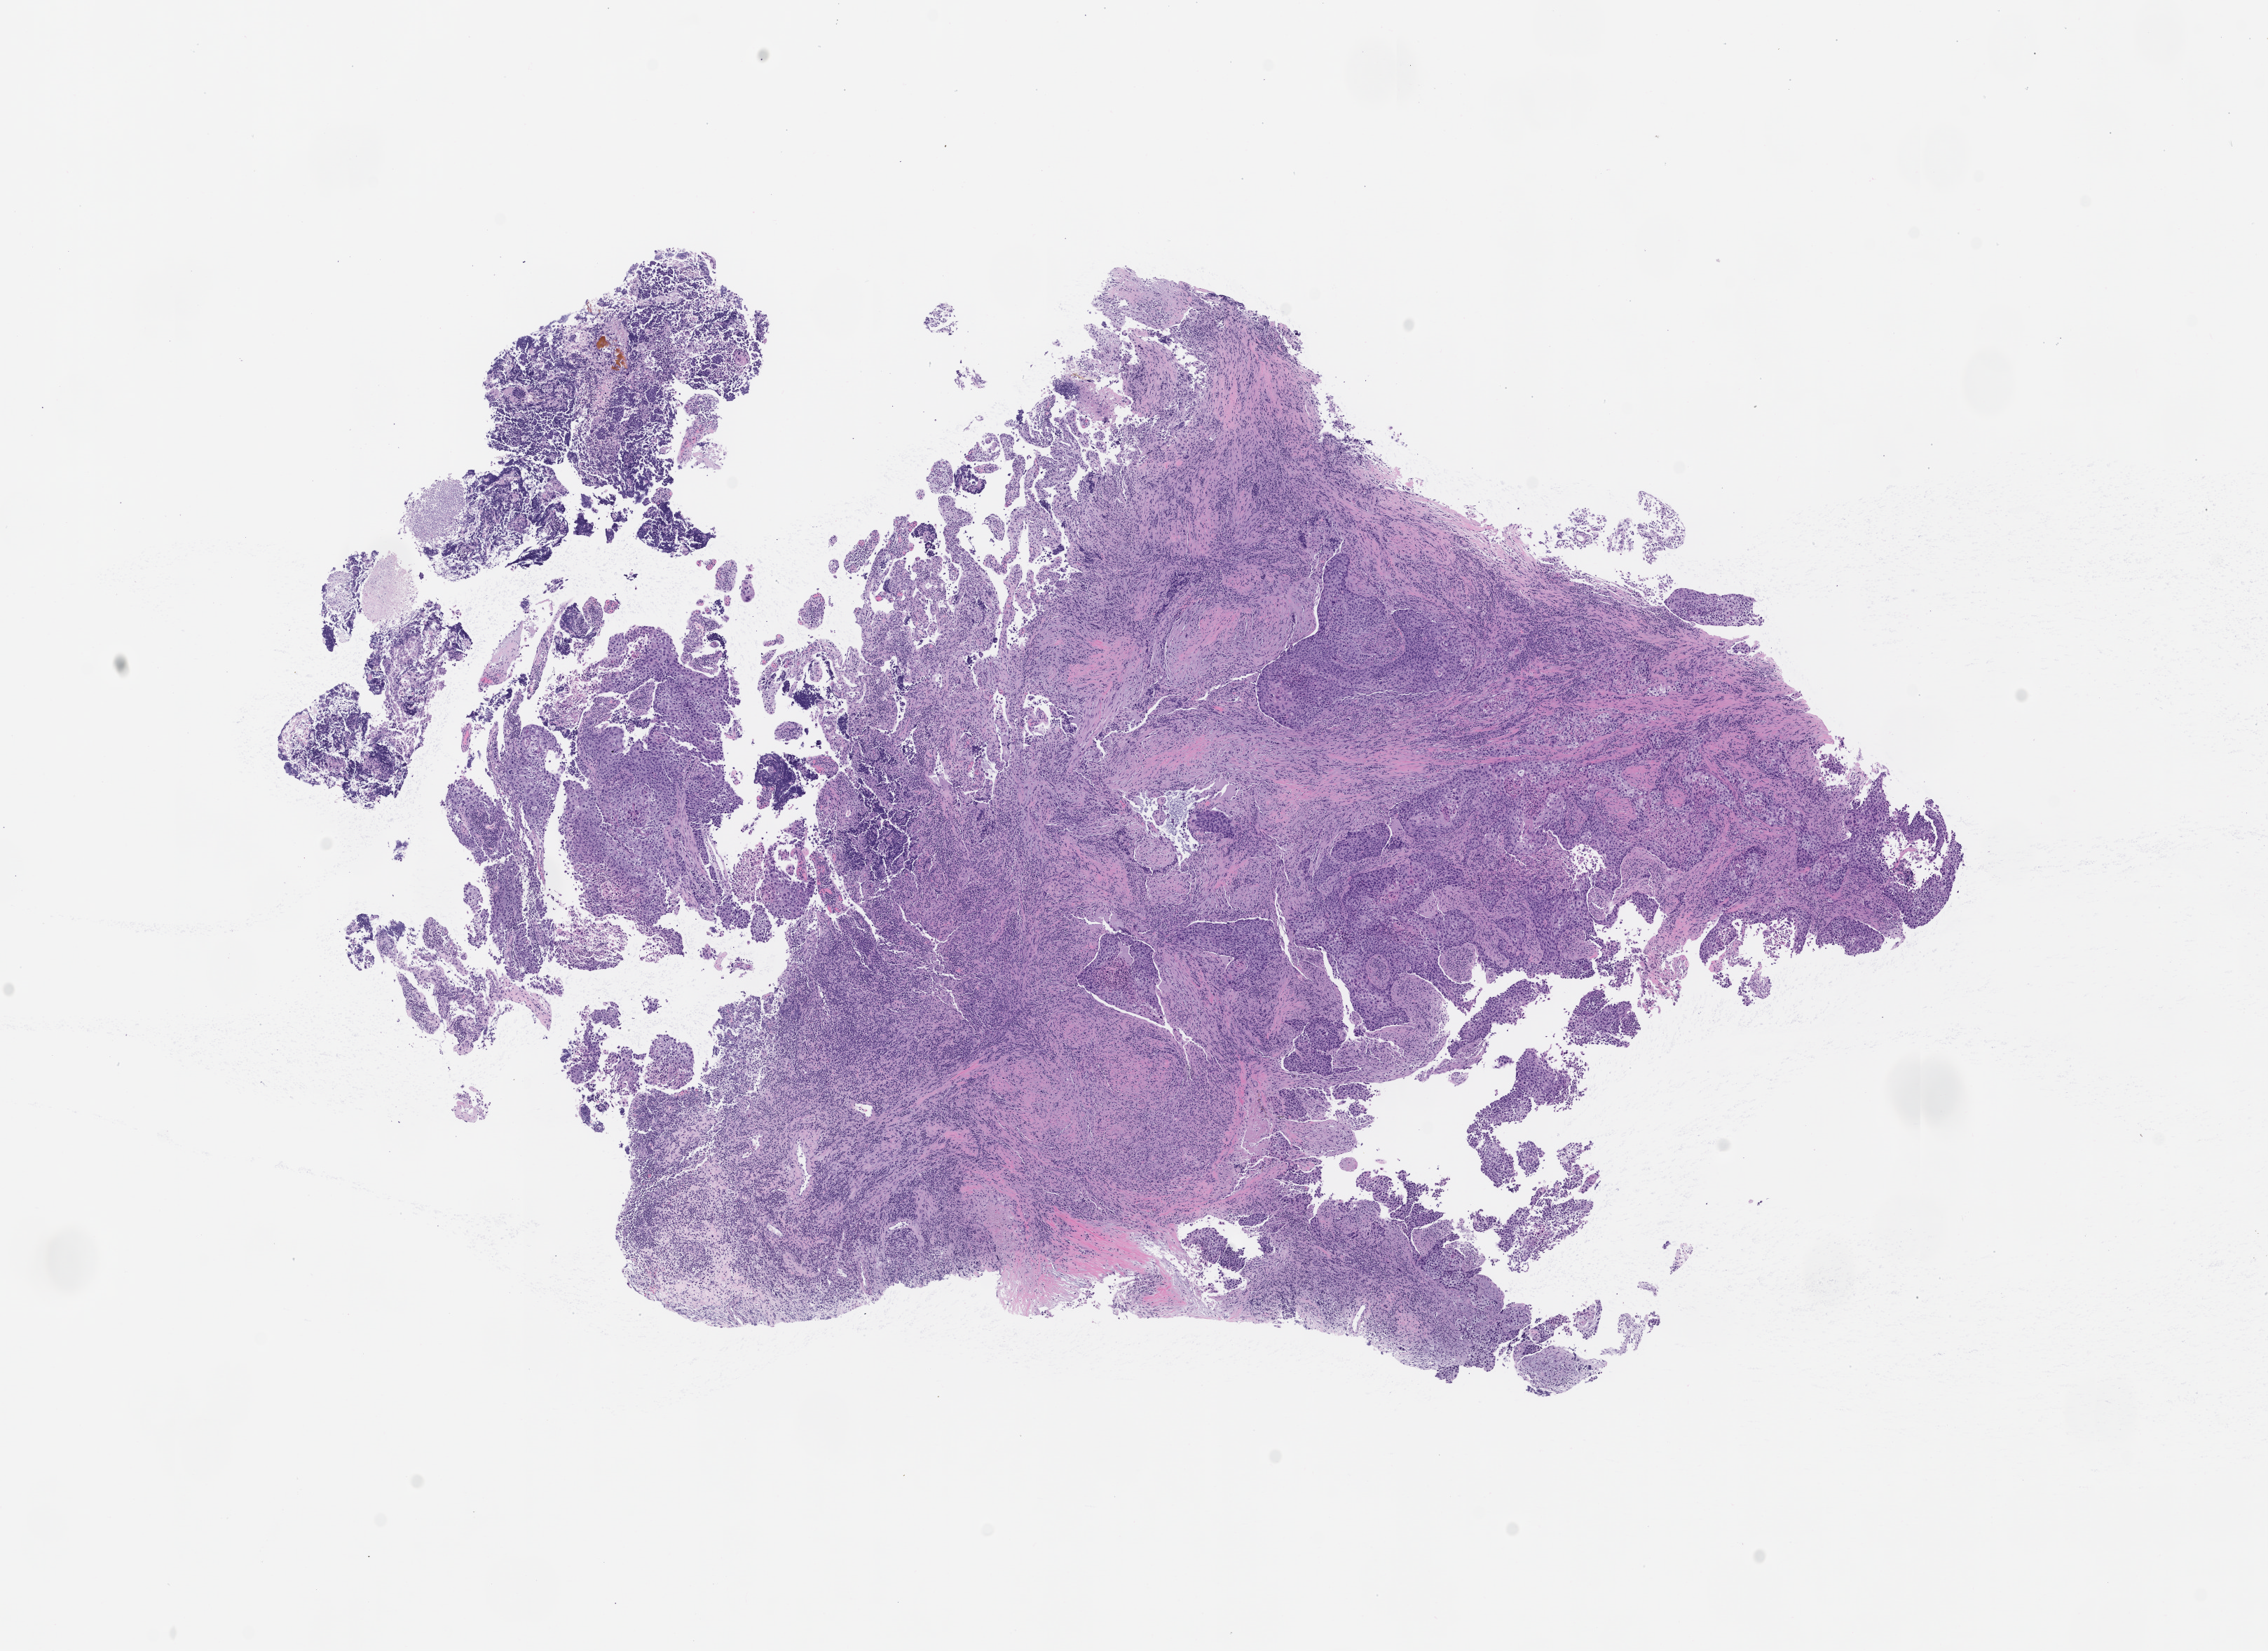
Digitized haematoxylin and eosin-stained section of the patient's (originator) tumor tissue, low-resolution overview of the scanned area, about 13.0 x 9.4 mm. Formalin-fixed, paraffin-embedded (FFPE) tissue. Tumor site category: bladder. Male patient, 73 years old.
- diagnosis: Urothelial Carcinoma